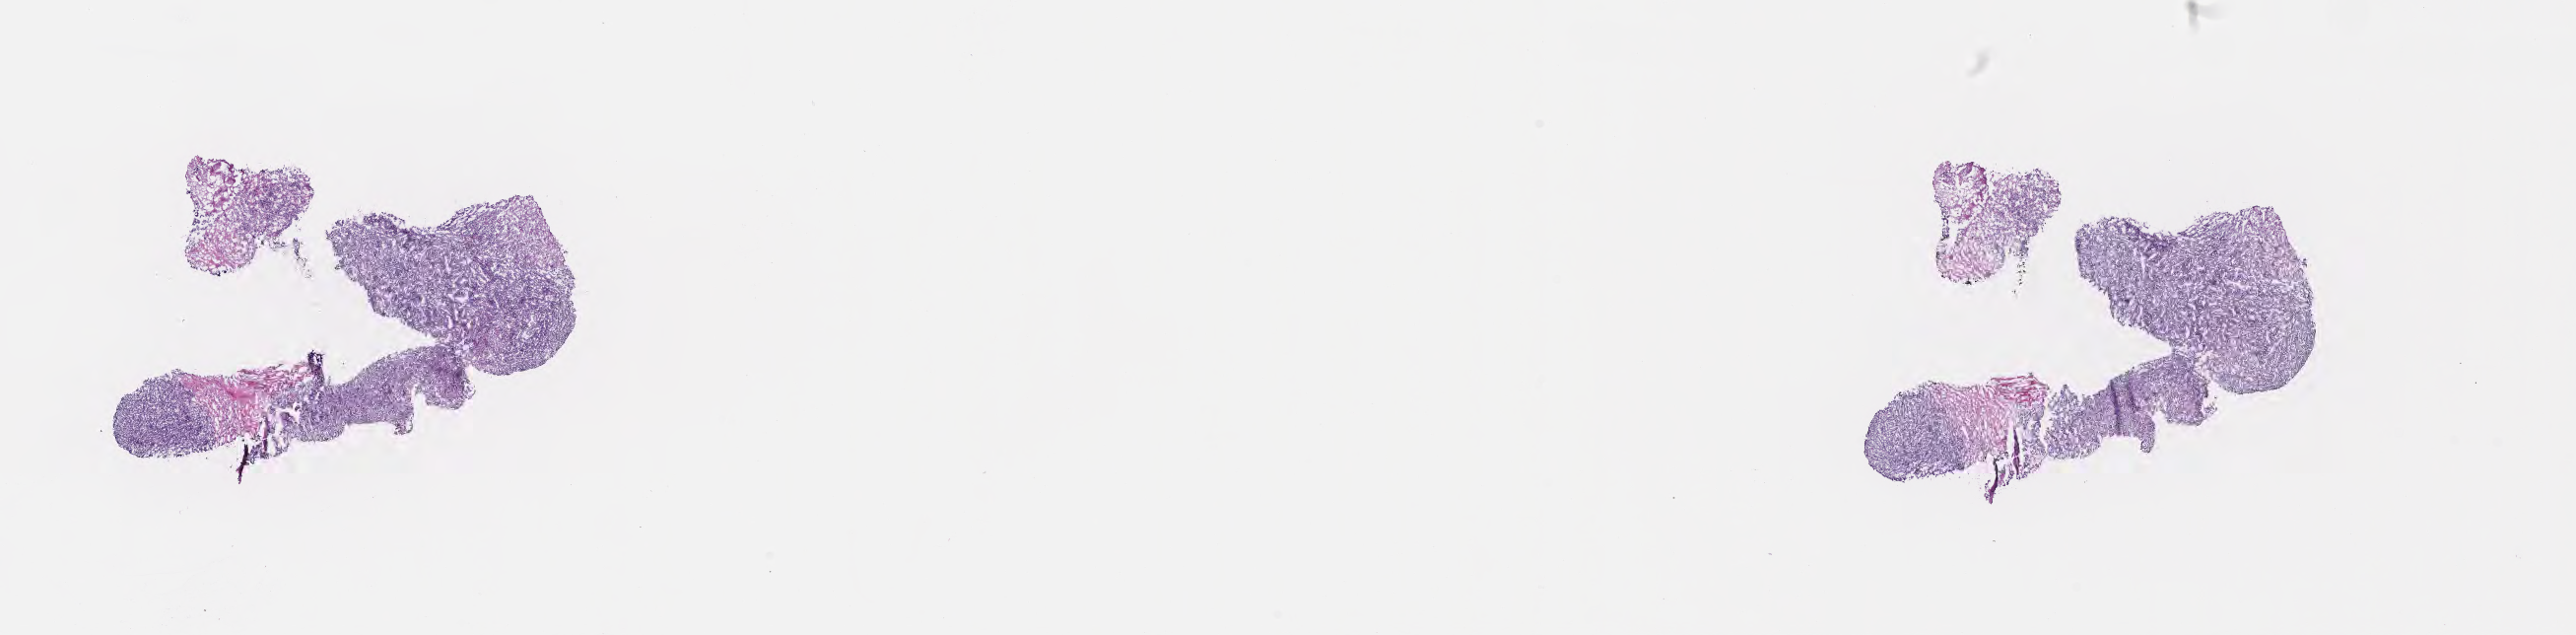
Whole-slide image, haematoxylin and eosin stain, a low-resolution overview of the entire scanned area, about 21.1 x 5.2 mm; cryosection; primary tumor. Patient: female, age at initial diagnosis 9 years. Pathologist review of this section (percent, as recorded): tumor cells 75%, tumor nuclei 85%, stromal cells 20%, necrosis 5%, normal cells 0%. Inflammatory infiltration, as recorded: lymphocyte infiltration 15%, monocyte infiltration 40%, neutrophil infiltration 5%.
Histologic diagnosis: Burkitt lymphoma, NOS. Ann Arbor stage (patient): Stage II.